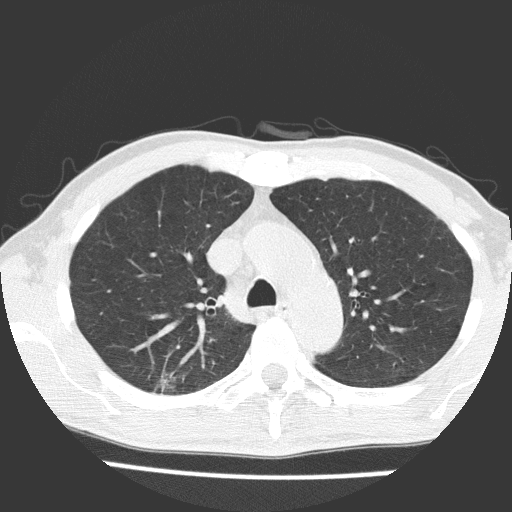
Low-dose screening chest CT, one axial slice; reconstruction kernel FC51; 120 kVp; lung window (W 1500 / L -600 HU); 2 mm slice thickness; 512 × 512 image matrix, field of view 309 × 309 mm.
Outlined on this slice (expert manual segmentation):
- lesion 1 (tumor, upper lobe of right lung): box from (x=157, y=376) to (x=176, y=392) px